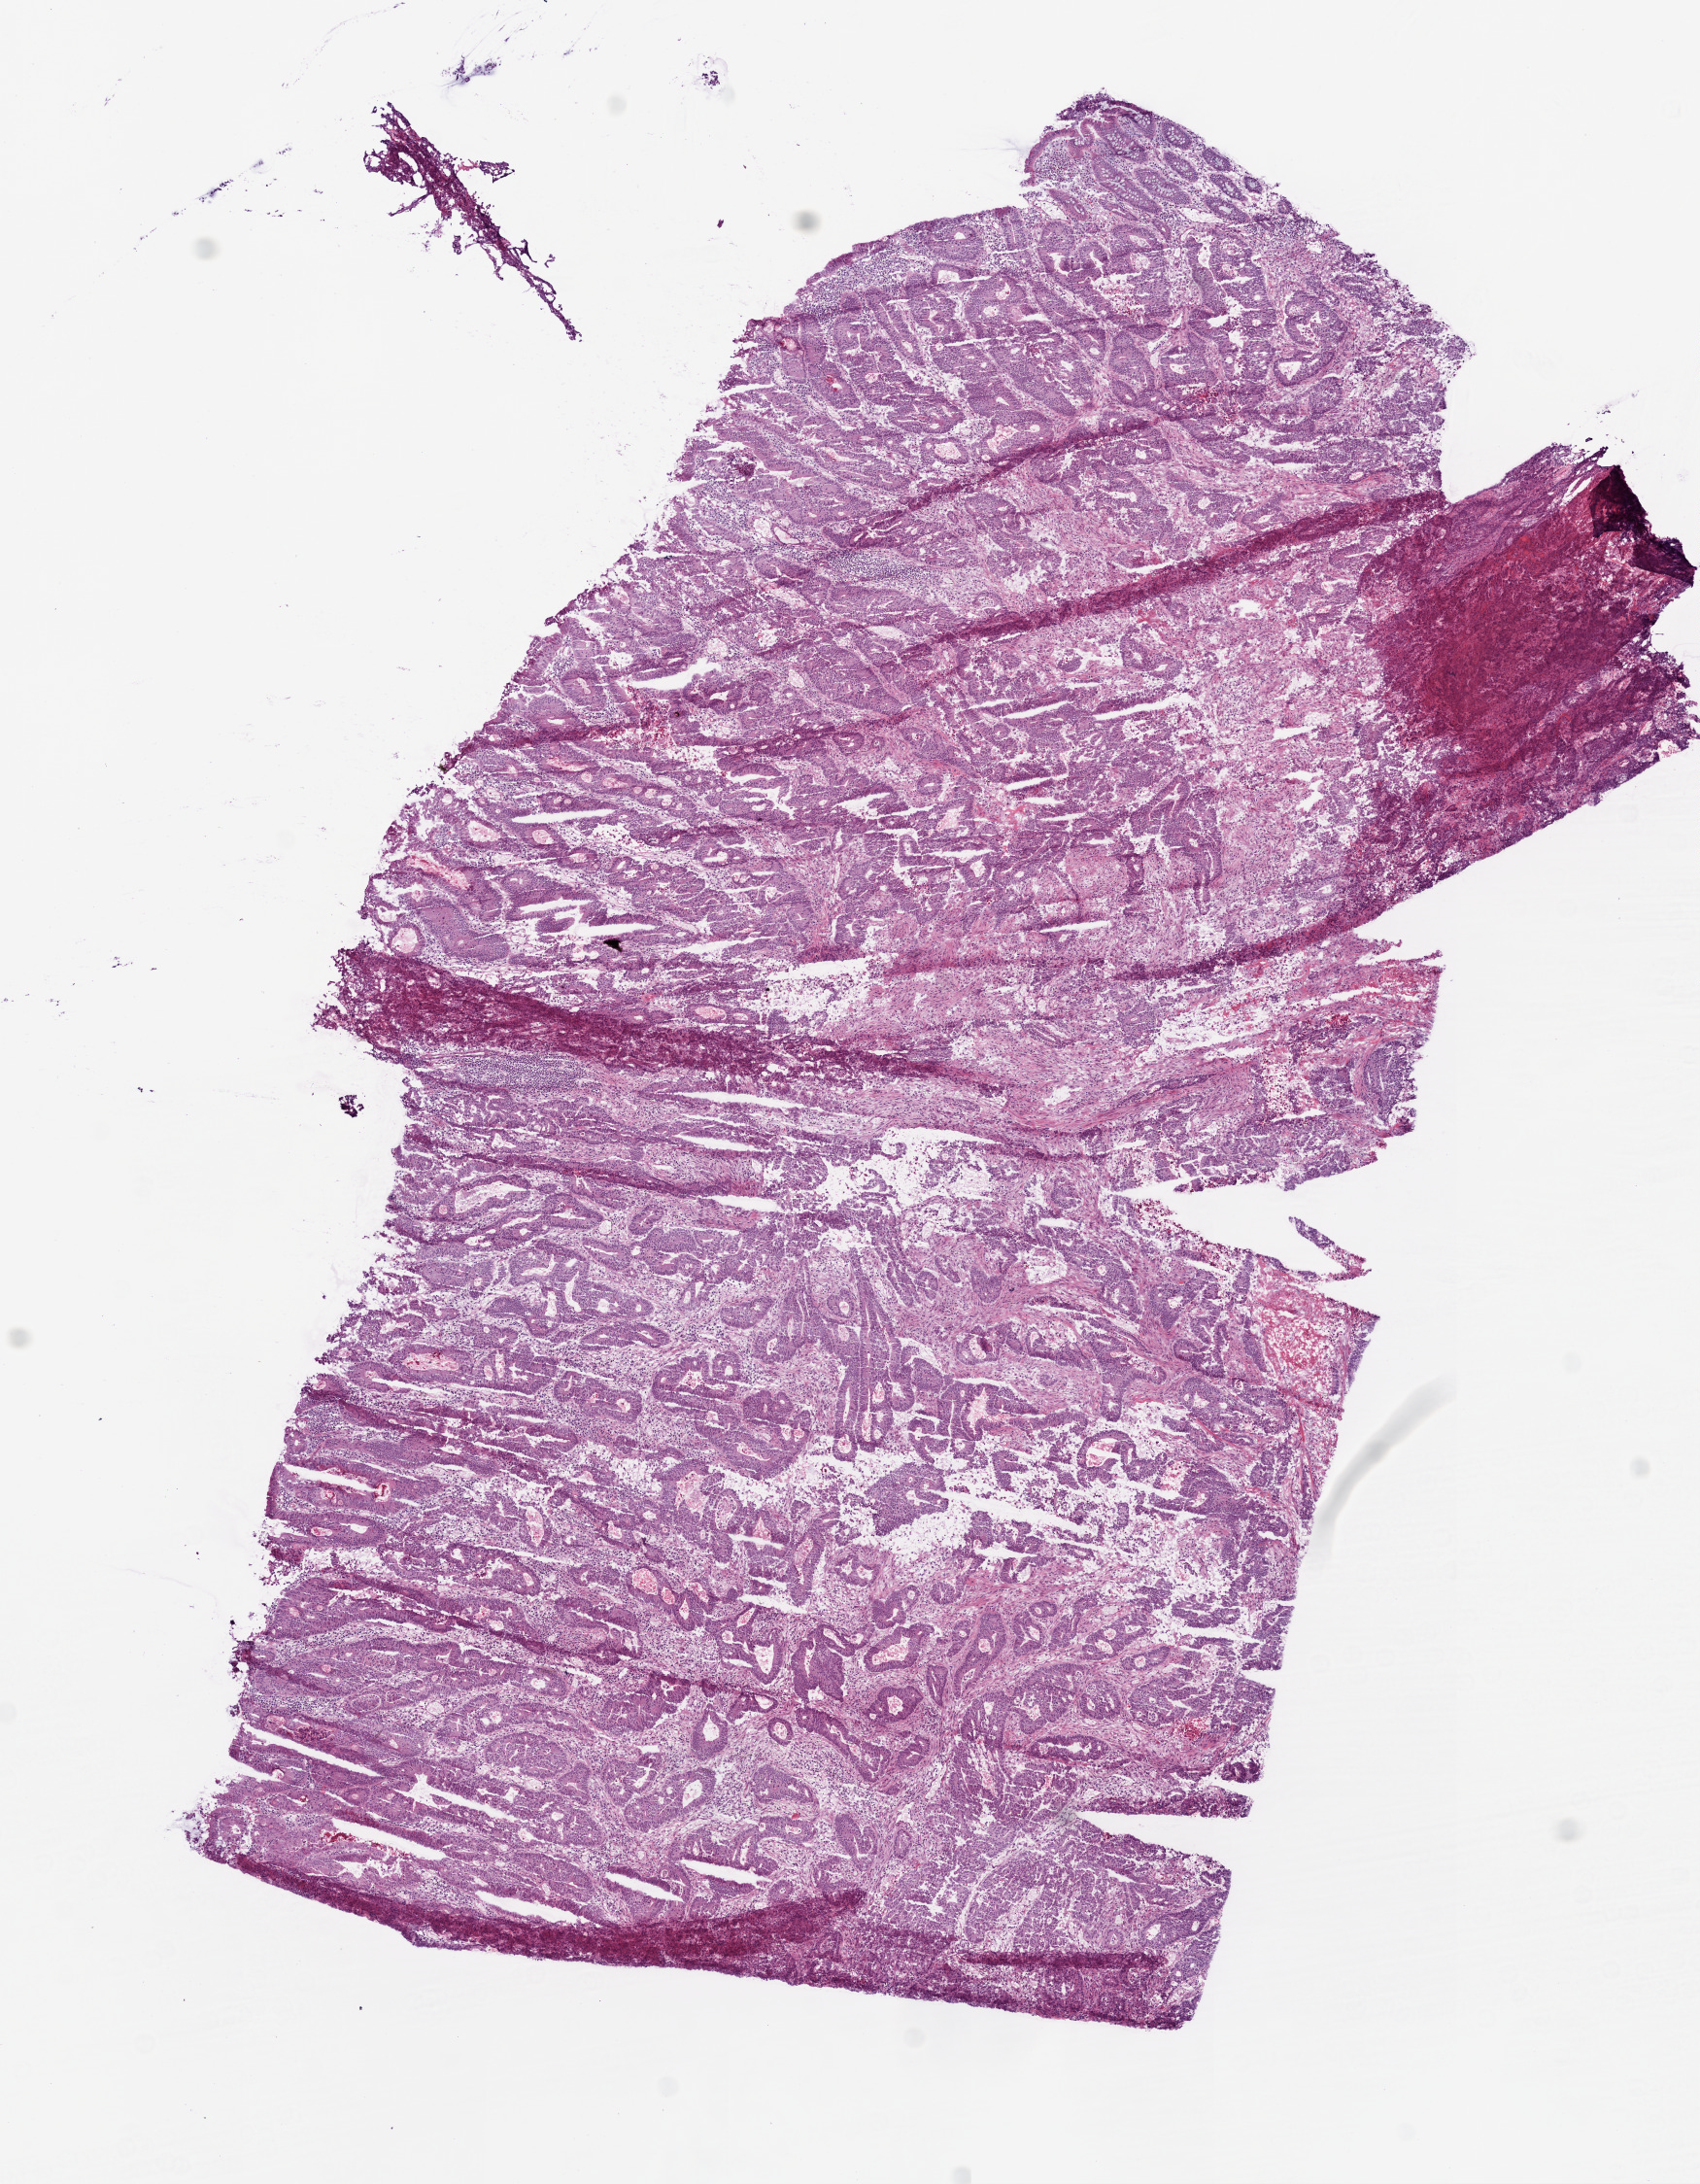
Whole-slide histology image, H&E-stained — shown as a low-resolution overview of the whole scanned area (about 7.0 x 9.0 mm, acquisition: 20x scan). Frozen section. Primary tumour sample from the colon. Patient: female, age at initial diagnosis 53 years. Slide review estimates, as recorded: tumour cells 80%, tumour nuclei 80%, normal cells 0%, stromal cells 10%, necrosis 10%.
Histologic diagnosis: Adenocarcinoma, NOS (sigmoid colon). AJCC pathologic stage: IIIB (6th edition). Lymph nodes positive (case pathology): 2 of 14 examined. TNM: T3 N1 M0.